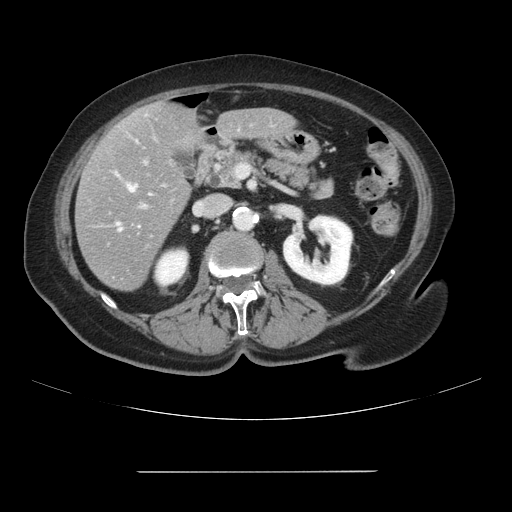
Contrast-enhanced abdominal CT, one axial slice. Slice 39 of 111 in the series (ordered by position). Intravenous contrast given. Soft-tissue window (W 400 / L 40 HU). 2.5 mm slice thickness. 512 × 512 image matrix. Female patient, age 74 years. Case-level facts recorded for this patient, not image findings: diagnosis: colorectal cancer liver metastases, imaged before liver resection; multiple liver metastases: yes; largest metastasis: 1.1 cm; disease in both lobes: yes.
Outlined on this slice (expert manual segmentation):
- hepatic veins: bounding box (x1, y1, x2, y2) in pixels: (117, 185, 136, 230)
- liver: (76, 103, 296, 291)
- planned liver remnant (the part of the liver to remain after resection): (140, 102, 295, 153)